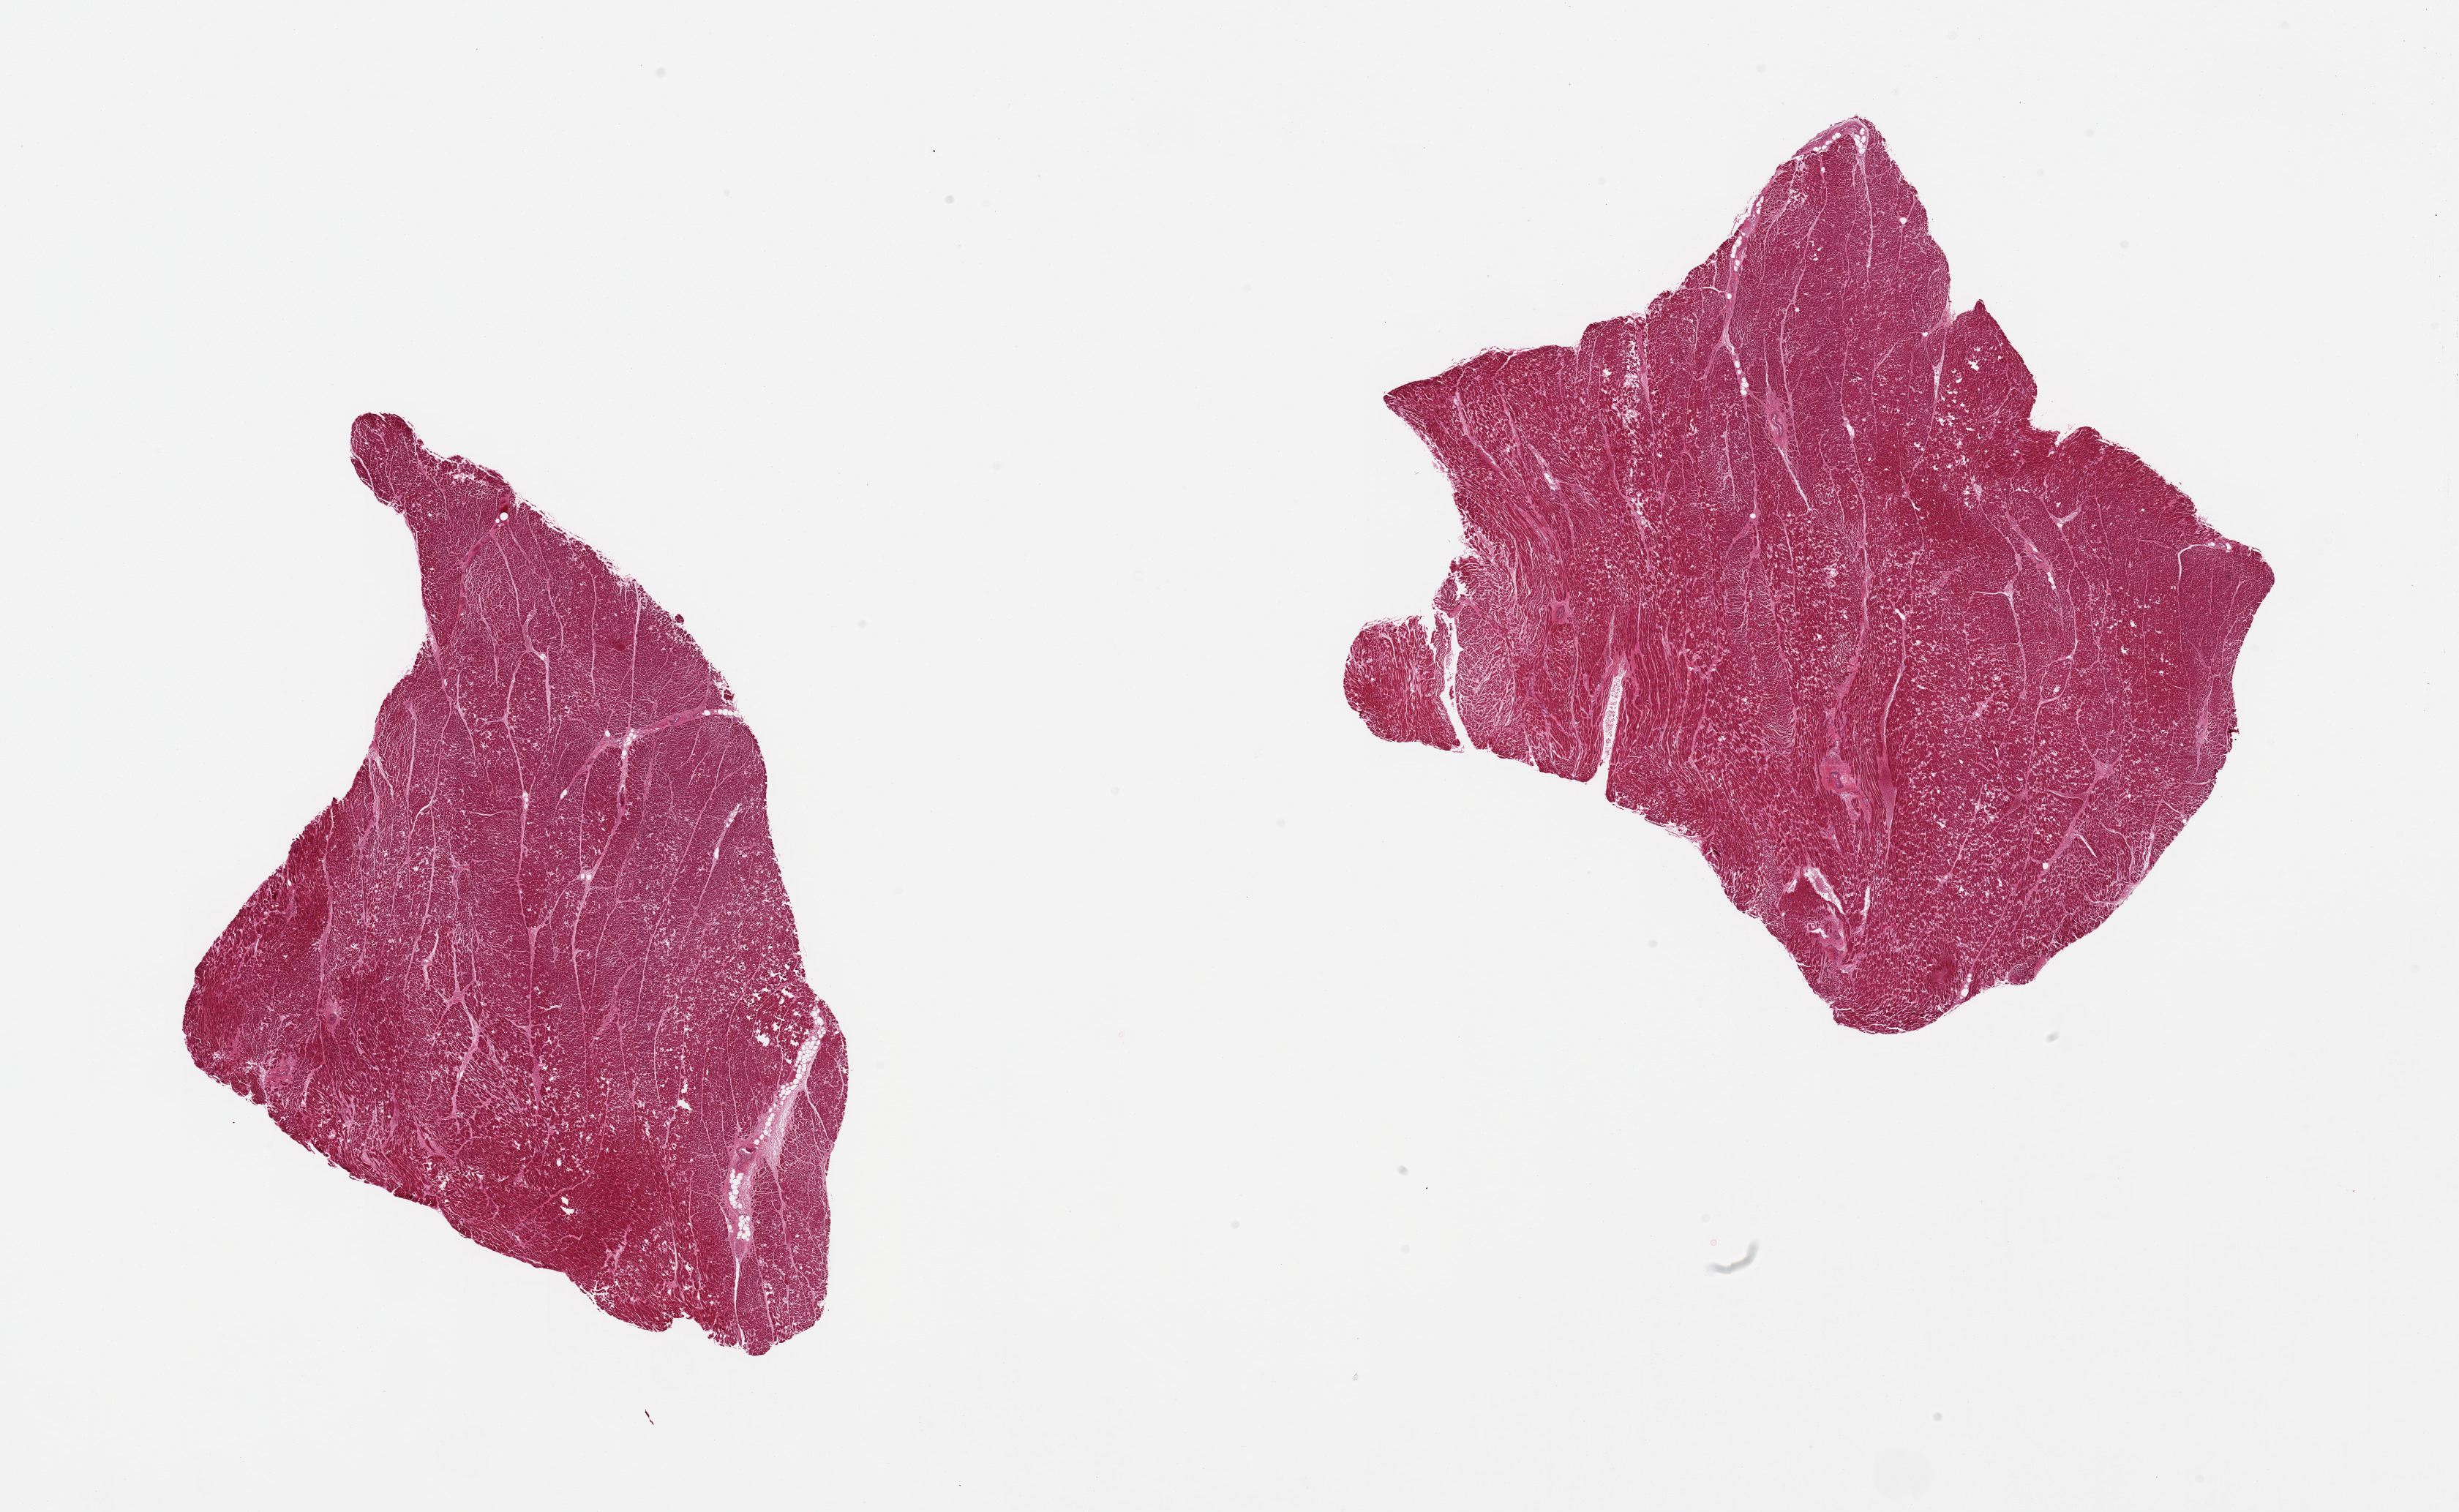
Digitized H&E-stained section, brightfield, shown as a low-resolution overview of the whole scanned area (about 26.6 x 16.3 mm, slide scanned at 20x); PAXgene-fixed paraffin-embedded (PFPE) section; sampled site (target tissue): heart; donor tissue sample. Male donor.
Reviewer comment on this tissue sample: 2 pieces.